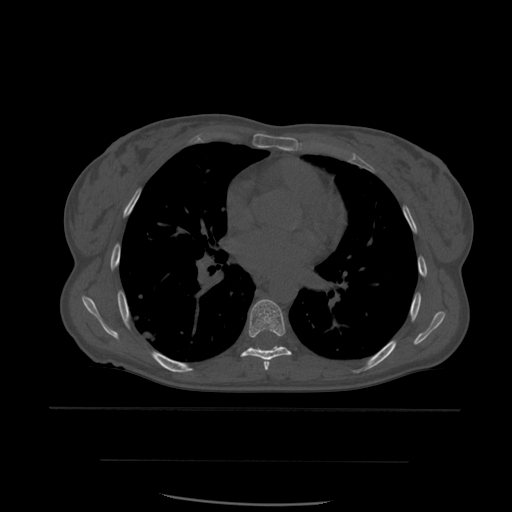
CT including the spine, one axial slice; position 374 of 574 along the scan axis; bone window (W 1800 / L 400 HU); 1.25 mm slice thickness; 512 × 512 image matrix, field of view 392 × 392 mm. Patient age 48 years. From the clinical record (not read from this slice): primary cancer: lung; vertebrae with lytic lesions (as recorded): T11.
Annotated regions visible in this slice (semi-automatically segmented with operator editing):
- T6 vertebra: bounding box <264,362,270,371> (left, top, right, bottom; pixels)
- T7 vertebra: <241,299,292,363>